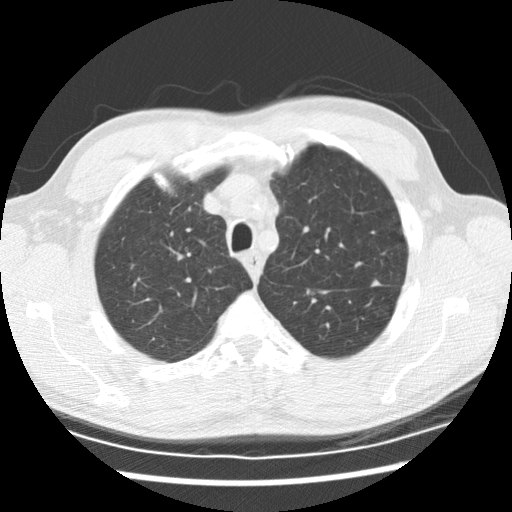
Low-dose screening chest CT, one axial slice. Slice 165 of 208 in the series (ordered by position). Reconstruction kernel STANDARD. Lung window (W 1500 / L -600 HU). 512 × 512 image matrix.
Outlined on this slice (manually delineated by an expert):
- lesion 3 (tumor, upper lobe of left lung): bounding box (x1, y1, x2, y2) in pixels: (371, 278, 382, 286)